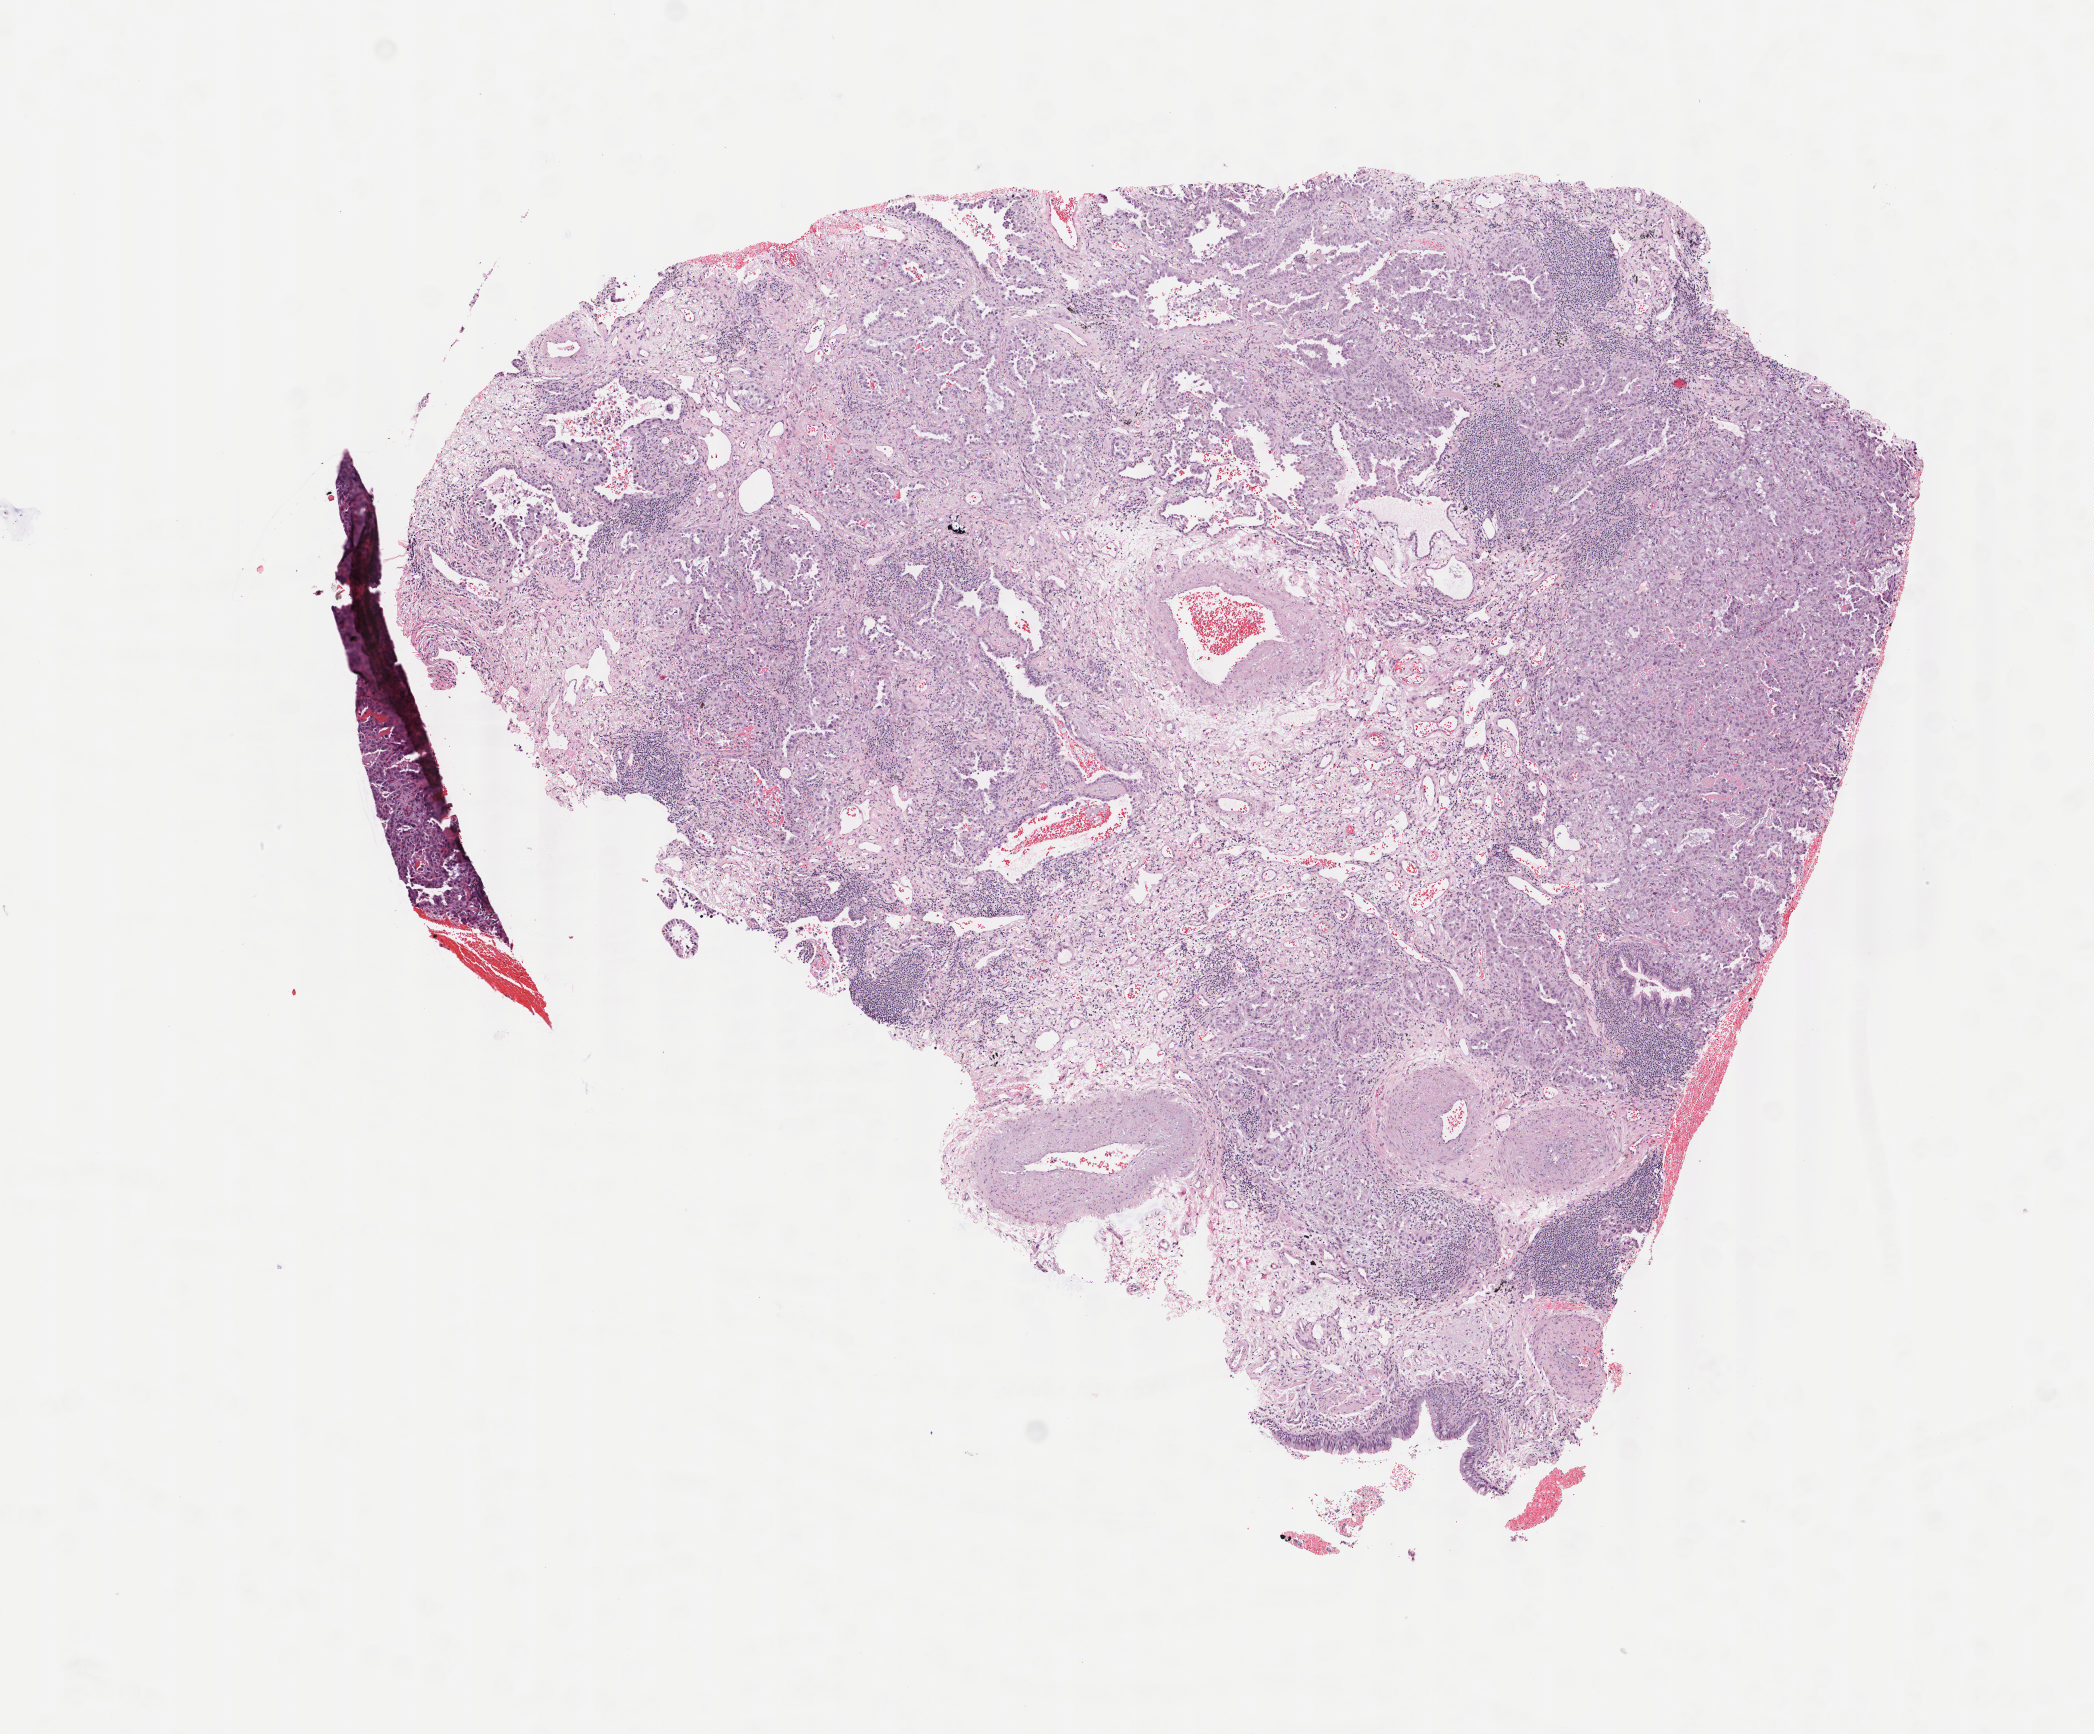
Whole-slide histology image, H&E-stained — whole scanned area (about 8.3 x 6.9 mm) shown as a low-resolution overview, frozen section from the bottom of the tissue portion, lung, primary tumour sample. Female patient; age at initial diagnosis 67 years. Composition of this section per pathologist review: tumour cells 55%, tumour nuclei 65%, normal cells 3%, stromal cells 42%, necrosis 0%. Infiltration values recorded for this section: lymphocyte infiltration 30%, monocyte infiltration 3%, neutrophil infiltration 2%.
* AJCC pathologic stage: IA (7th edition)
* histologic diagnosis: Adenocarcinoma, NOS (upper lobe, lung)
* laterality: right
* TNM: T1b NX M0